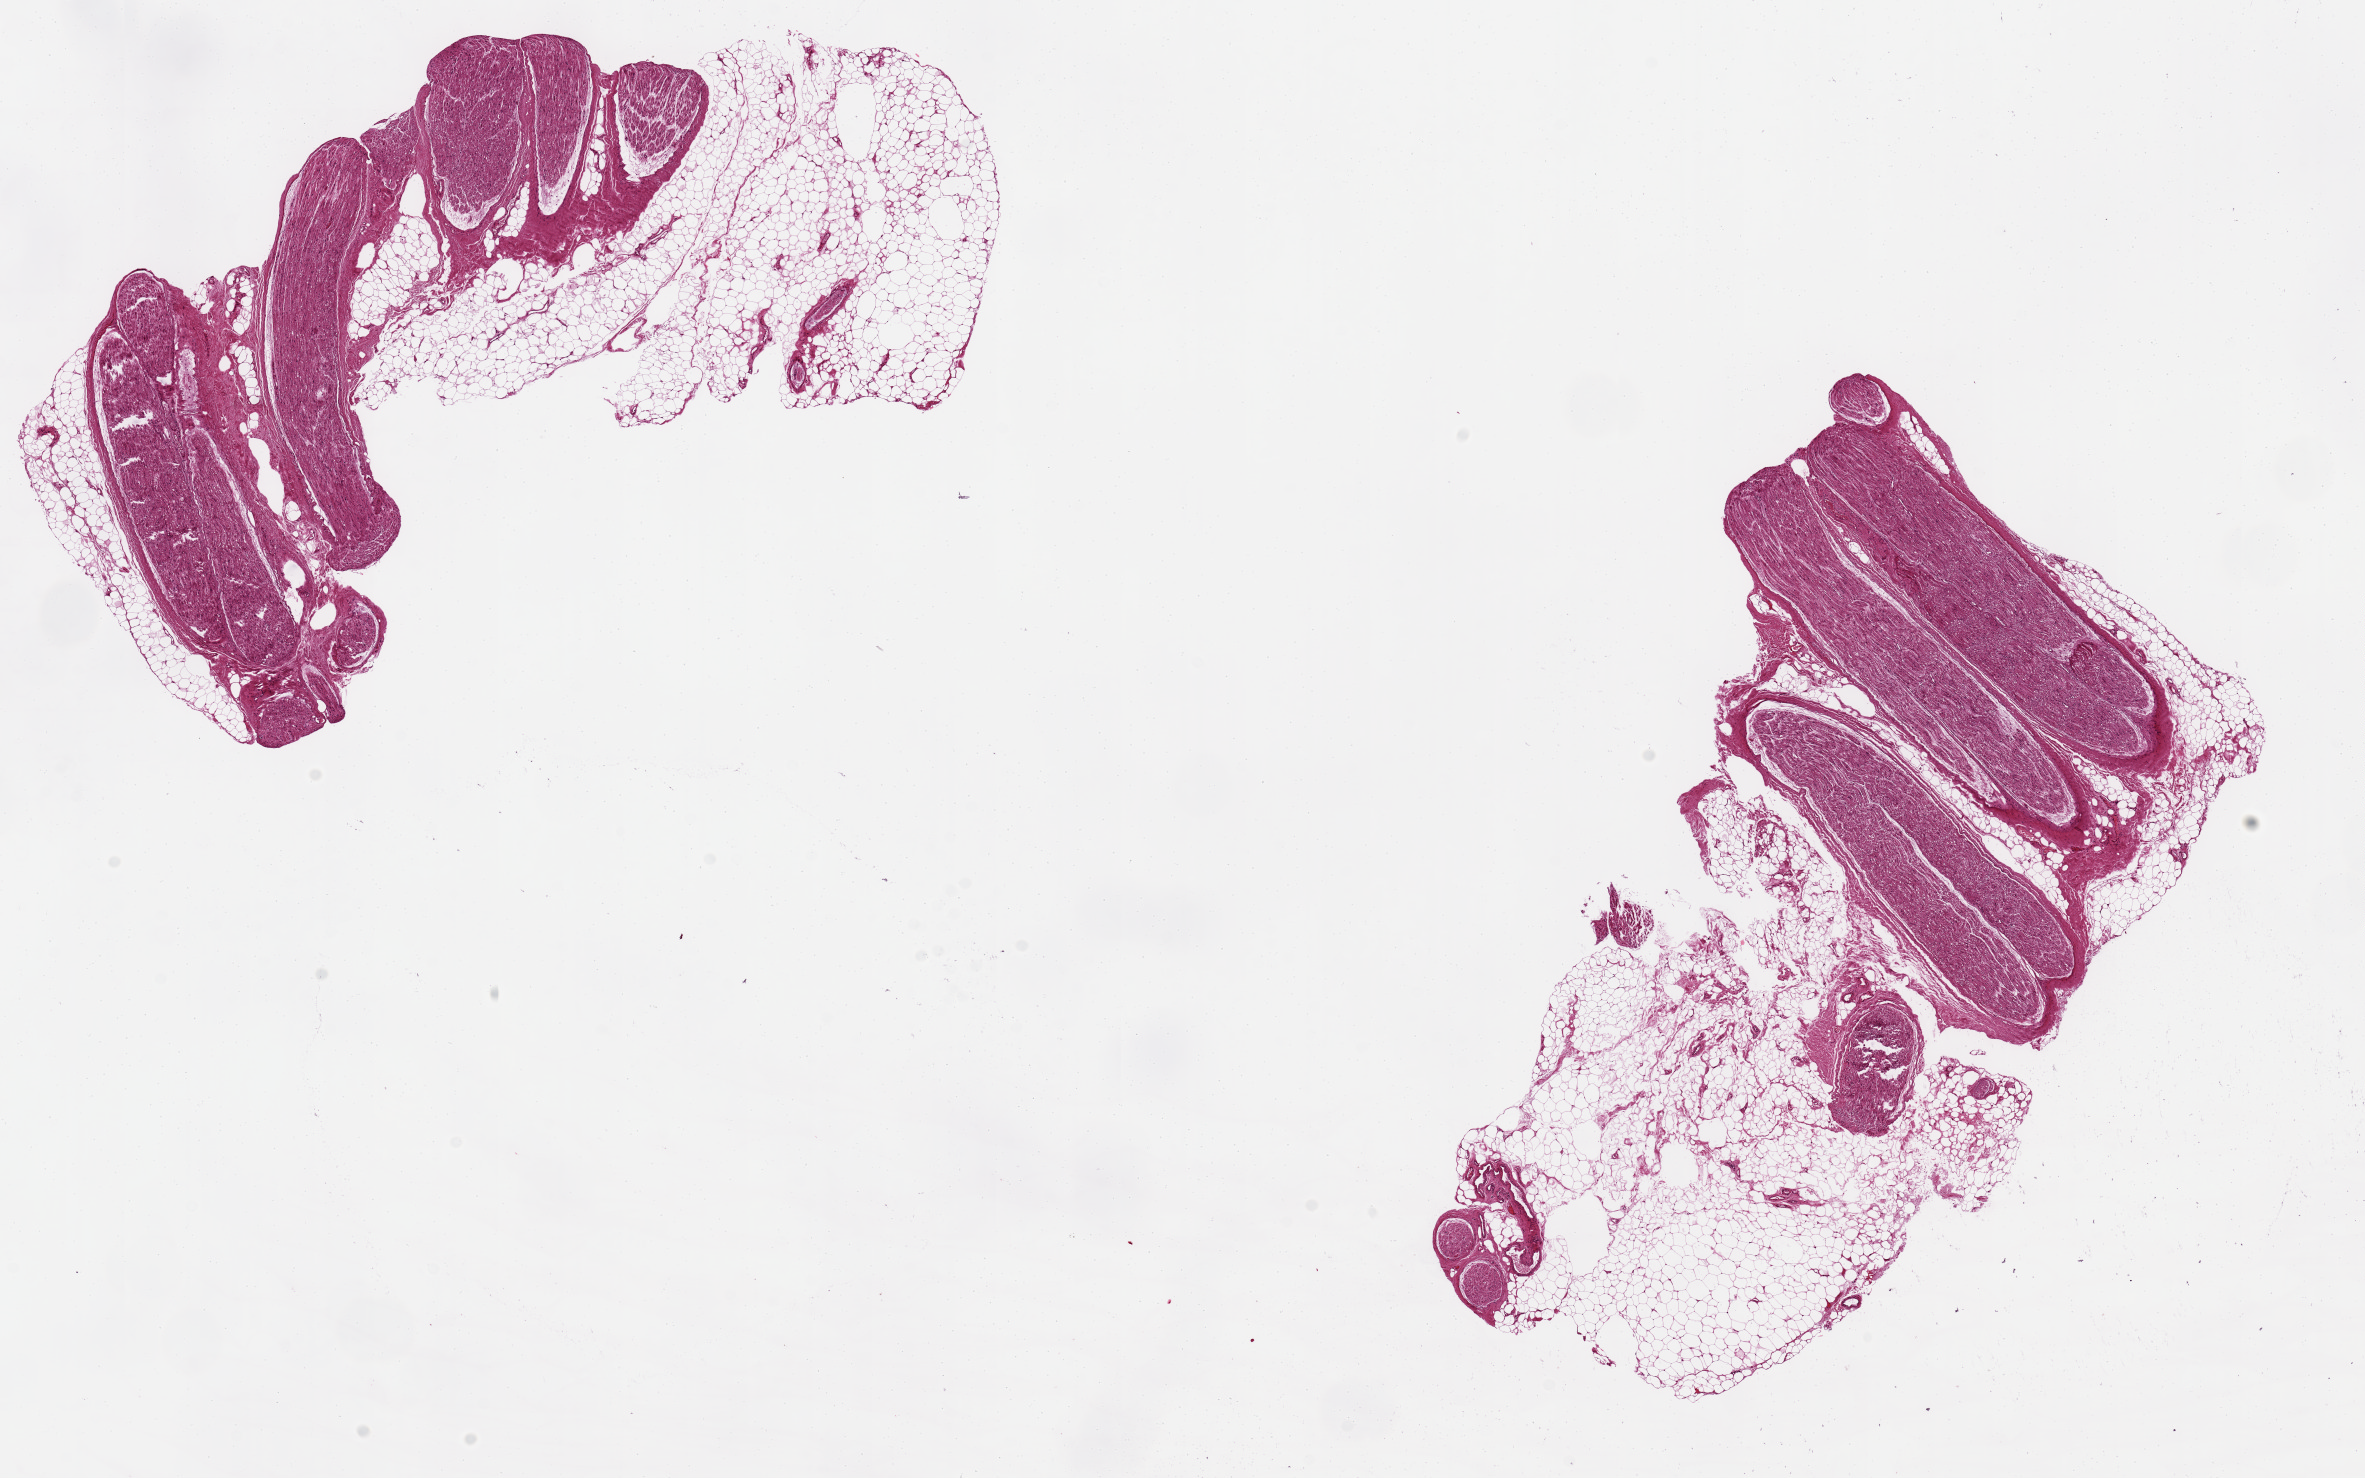
Whole-slide image, hematoxylin and eosin (H&E) stain — whole scanned area (about 18.7 x 11.7 mm) shown as a low-resolution overview, PAXgene-fixed, paraffin-embedded tissue, target tissue: tibial nerve, donor tissue sample. Donor: female.
Pathologist's review note for this sample: Widespread vacuolar degeneration. 2 pieces: 4.6x7.4mm. 50% fat.